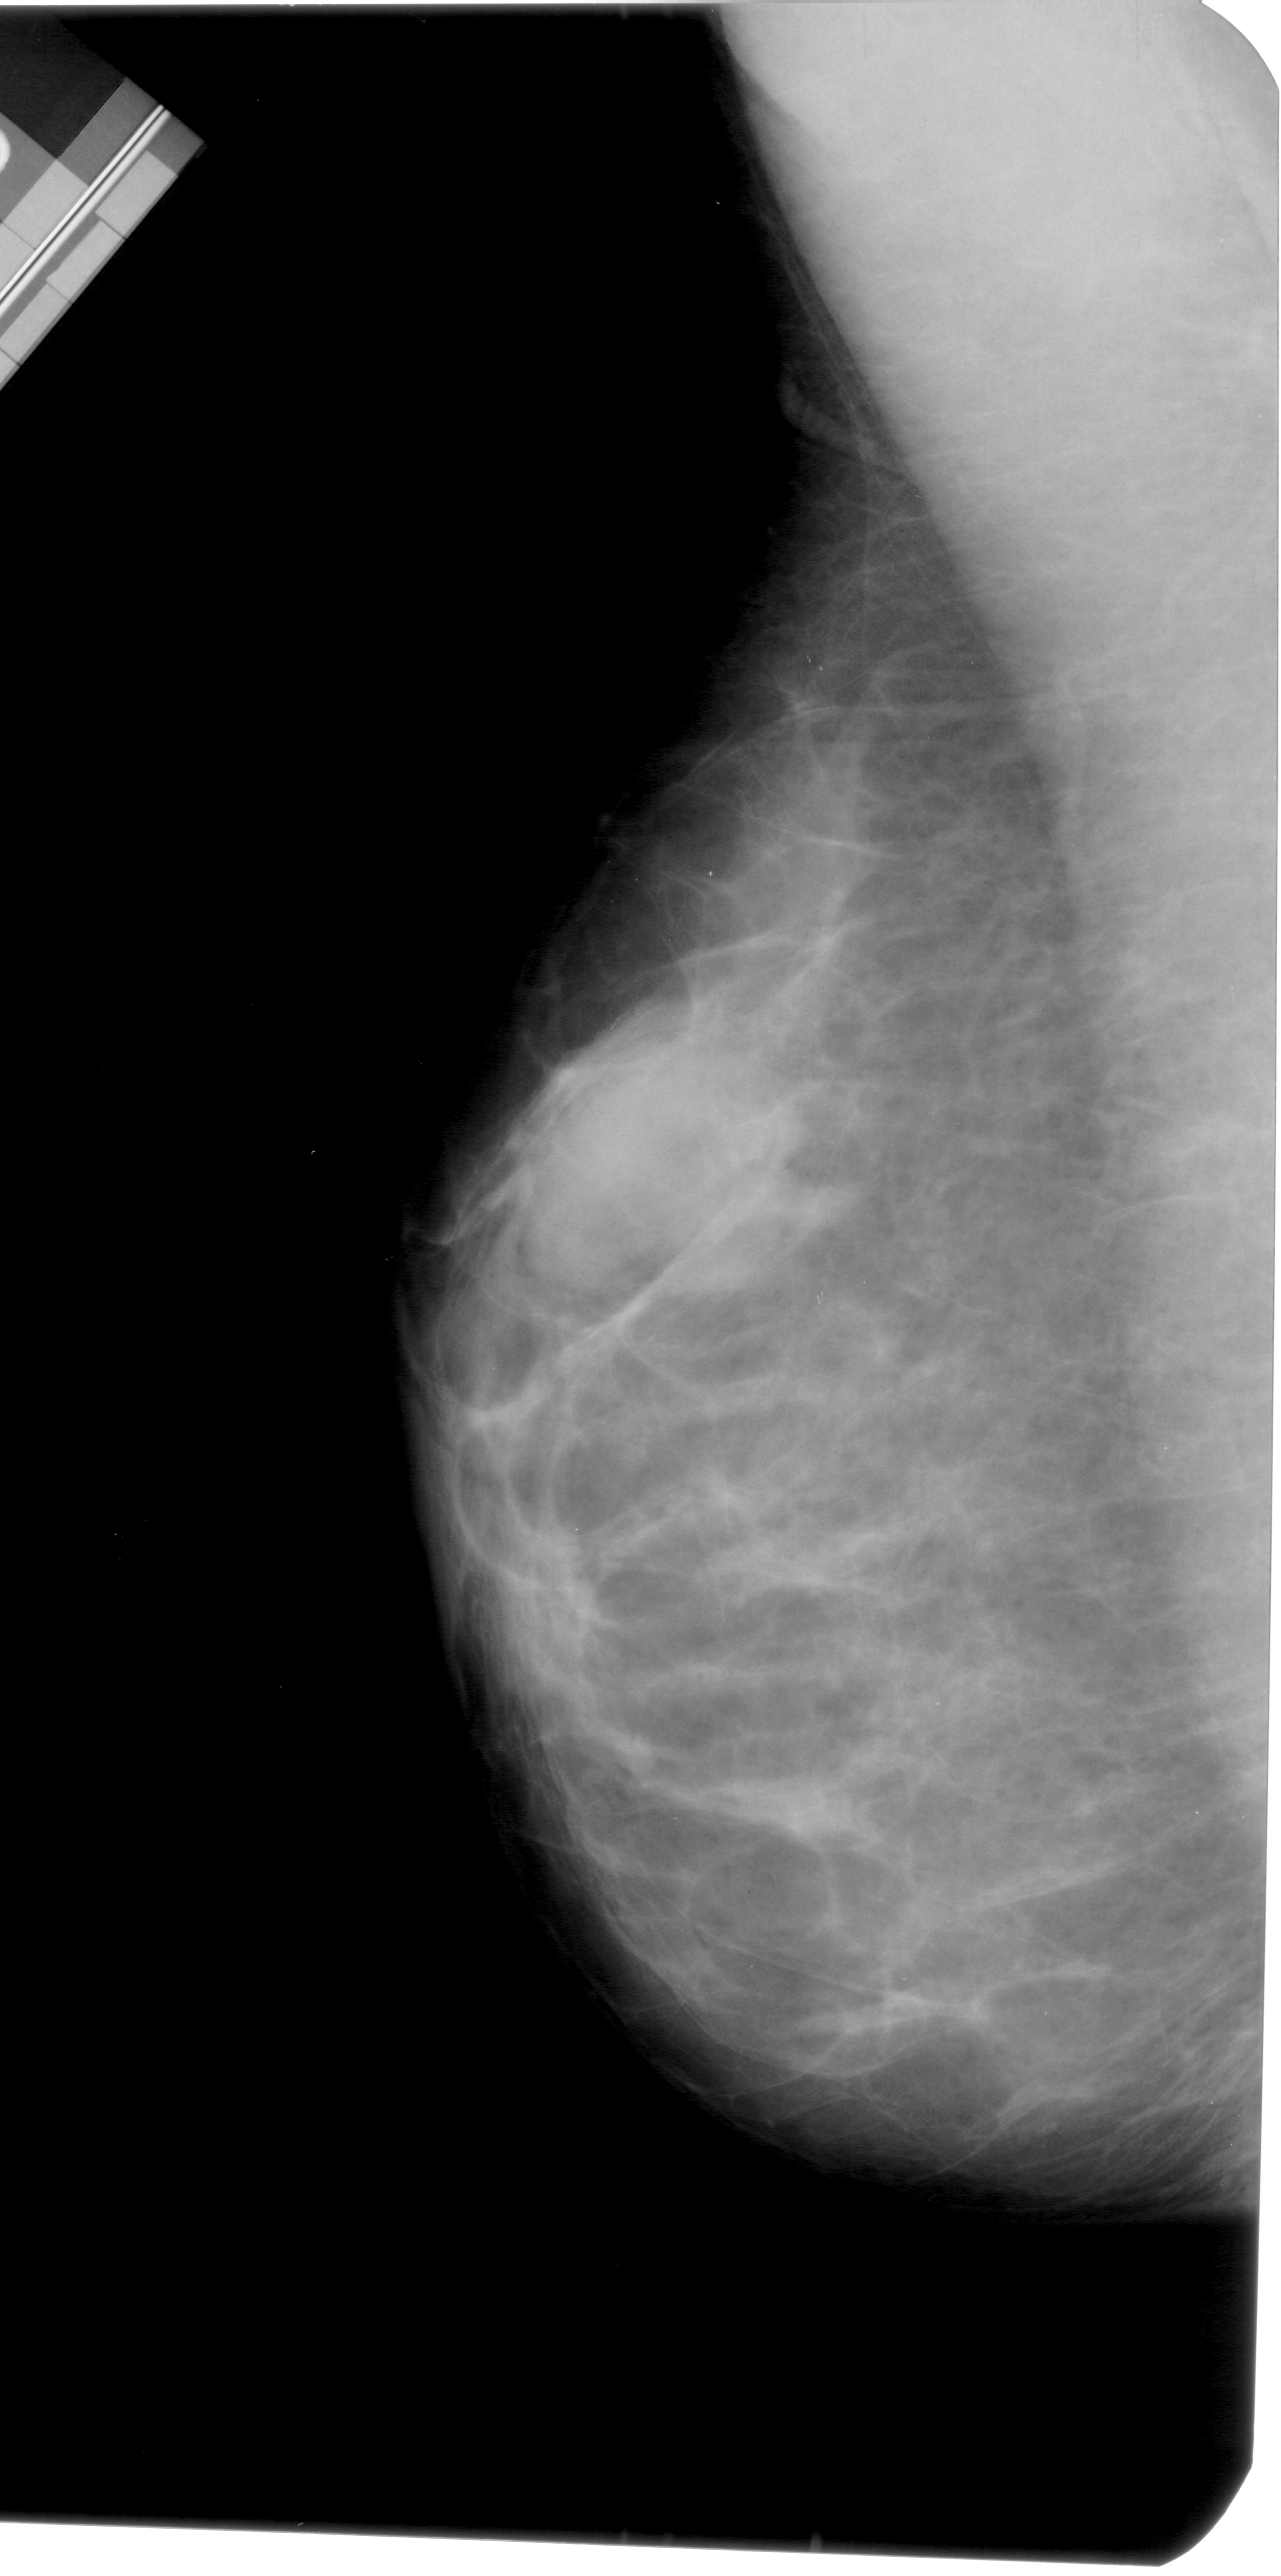
Digitized screen-film mammogram; left breast; mediolateral oblique (MLO) view; breast composition: extremely dense (BI-RADS density category 4 of 4); 1281 × 2576 image matrix.
Marked abnormalities (boxes around the expert regions of interest):
- mass, shape oval, margins obscured; BI-RADS assessment category 4; pathology (as recorded): benign: bounding box (x1, y1, x2, y2) in pixels: (484, 996, 715, 1244)